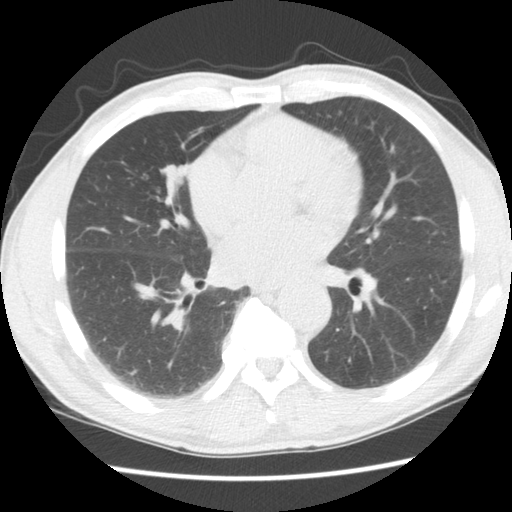
Chest CT (low-dose screening protocol), one axial image, second screening round (one year after baseline), lung window (W 1500 / L -600 HU), standard (soft-tissue) reconstruction kernel (STANDARD), 120 kVp, slice 82 of 152 in the series, 512 × 512 image matrix, field of view 337 × 337 mm. Male, age 65 years at enrolment. Current smoker at enrolment.
Lesion marked by an expert reader, box from (x=135, y=153) to (x=198, y=209) px. Reader record for this screening exam (exam-level; its link to the box is not recorded): non-calcified nodule or mass ≥4 mm, right middle lobe, 11 × 9 mm, smooth margins, soft tissue attenuation, pre-existing on the prior screen: no. Lung cancer was diagnosed 601 days after this screen (after the third annual screen): squamous cell carcinoma, NOS, right middle lobe, poorly differentiated (G3), stage IA (AJCC 6th edition), 23 mm at pathology.